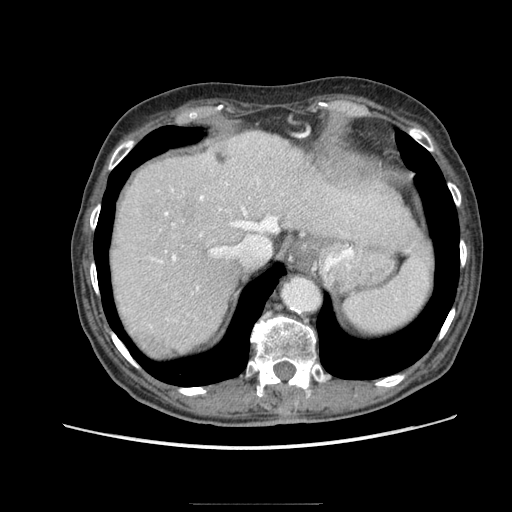
Contrast-enhanced abdominal CT (liver protocol), one axial slice; slice 67 of 83 in the series (ordered by position); reconstruction kernel STANDARD; soft-tissue window (W 400 / L 40 HU); 512 × 512 image matrix. Case-level facts recorded for this patient, not image findings: diagnosis: hepatocellular carcinoma (patient treated with transarterial chemoembolisation; whether this scan precedes or follows treatment is not stated here); TNM stage (as recorded): Stage-I; Child-Pugh class: A; tumour differentiation: moderately differentiated; tumour nodularity: uninodular.
Outlined on this slice (semi-automatic segmentation, software-assisted and operator-edited):
- abdominal aorta: bounding box <282,278,320,313> (left, top, right, bottom; pixels)
- liver parenchyma outside the tumour (the mass and vessels are separate outlines, so this box may not span the whole liver): <110,130,383,354>
- mass: <149,337,168,356>
- liver vessels: <151,183,277,290>